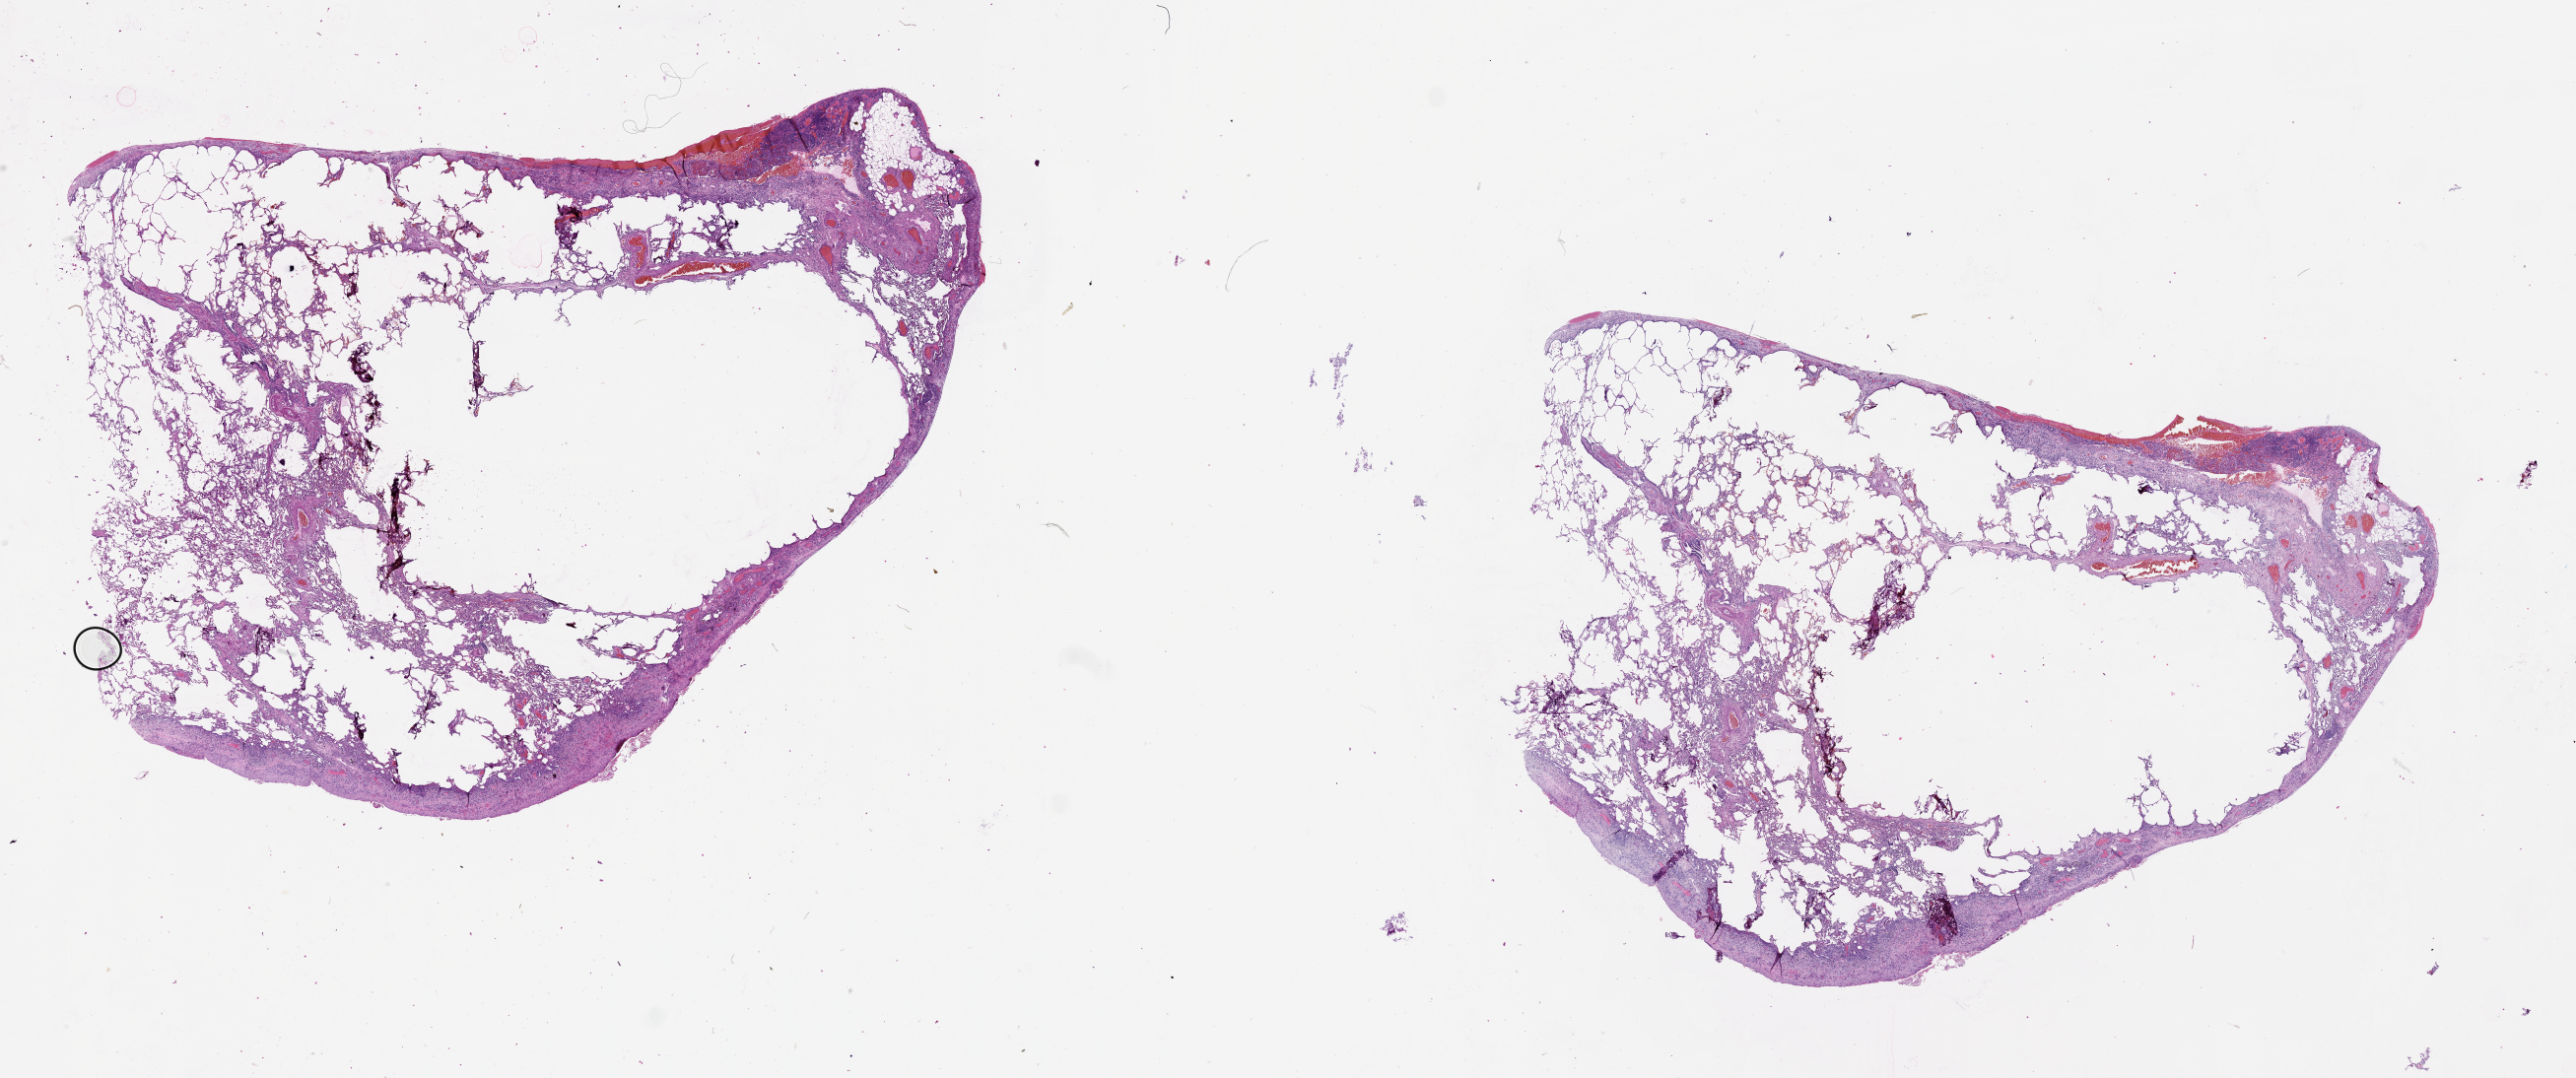
H&E whole-slide image, low-resolution overview of the scanned area, about 42.1 x 17.6 mm (acquisition: 20x scan), normal (non-tumour) tissue sample, lung. Male, 49 y/o.
This section: normal (non-tumour) tissue from the same patient. Patient diagnosis (cohort enrolment): squamous cell carcinoma (lung).